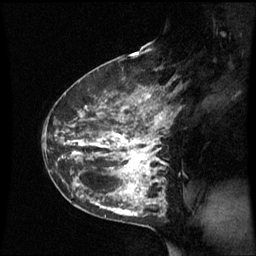
Breast MRI (dynamic contrast-enhanced), one sagittal slice; slice 35 of 60 in the series (ordered by position); dynamic contrast-enhanced series, image 2 of 3 at this slice position (ordered by acquisition); 1.5 T; TE 4.2 ms, TR 8.9 ms; 2.4 mm slice thickness; 256 × 256 image matrix. Patient: female, 42 years. Case-level facts recorded for this patient, not image findings: setting: breast cancer imaged before/during neoadjuvant chemotherapy; receptor status: HER2-positive.
Structures marked on this image (semi-automatically segmented with operator editing):
- analysis volume of interest (the breast-tissue region the enhancement analysis was run in; not a lesion): box from (x=62, y=93) to (x=167, y=210) px
- tumour enhancement mask (voxels above the 70 % enhancement threshold inside the analysis volume of interest): (x=68, y=95)–(x=164, y=199)